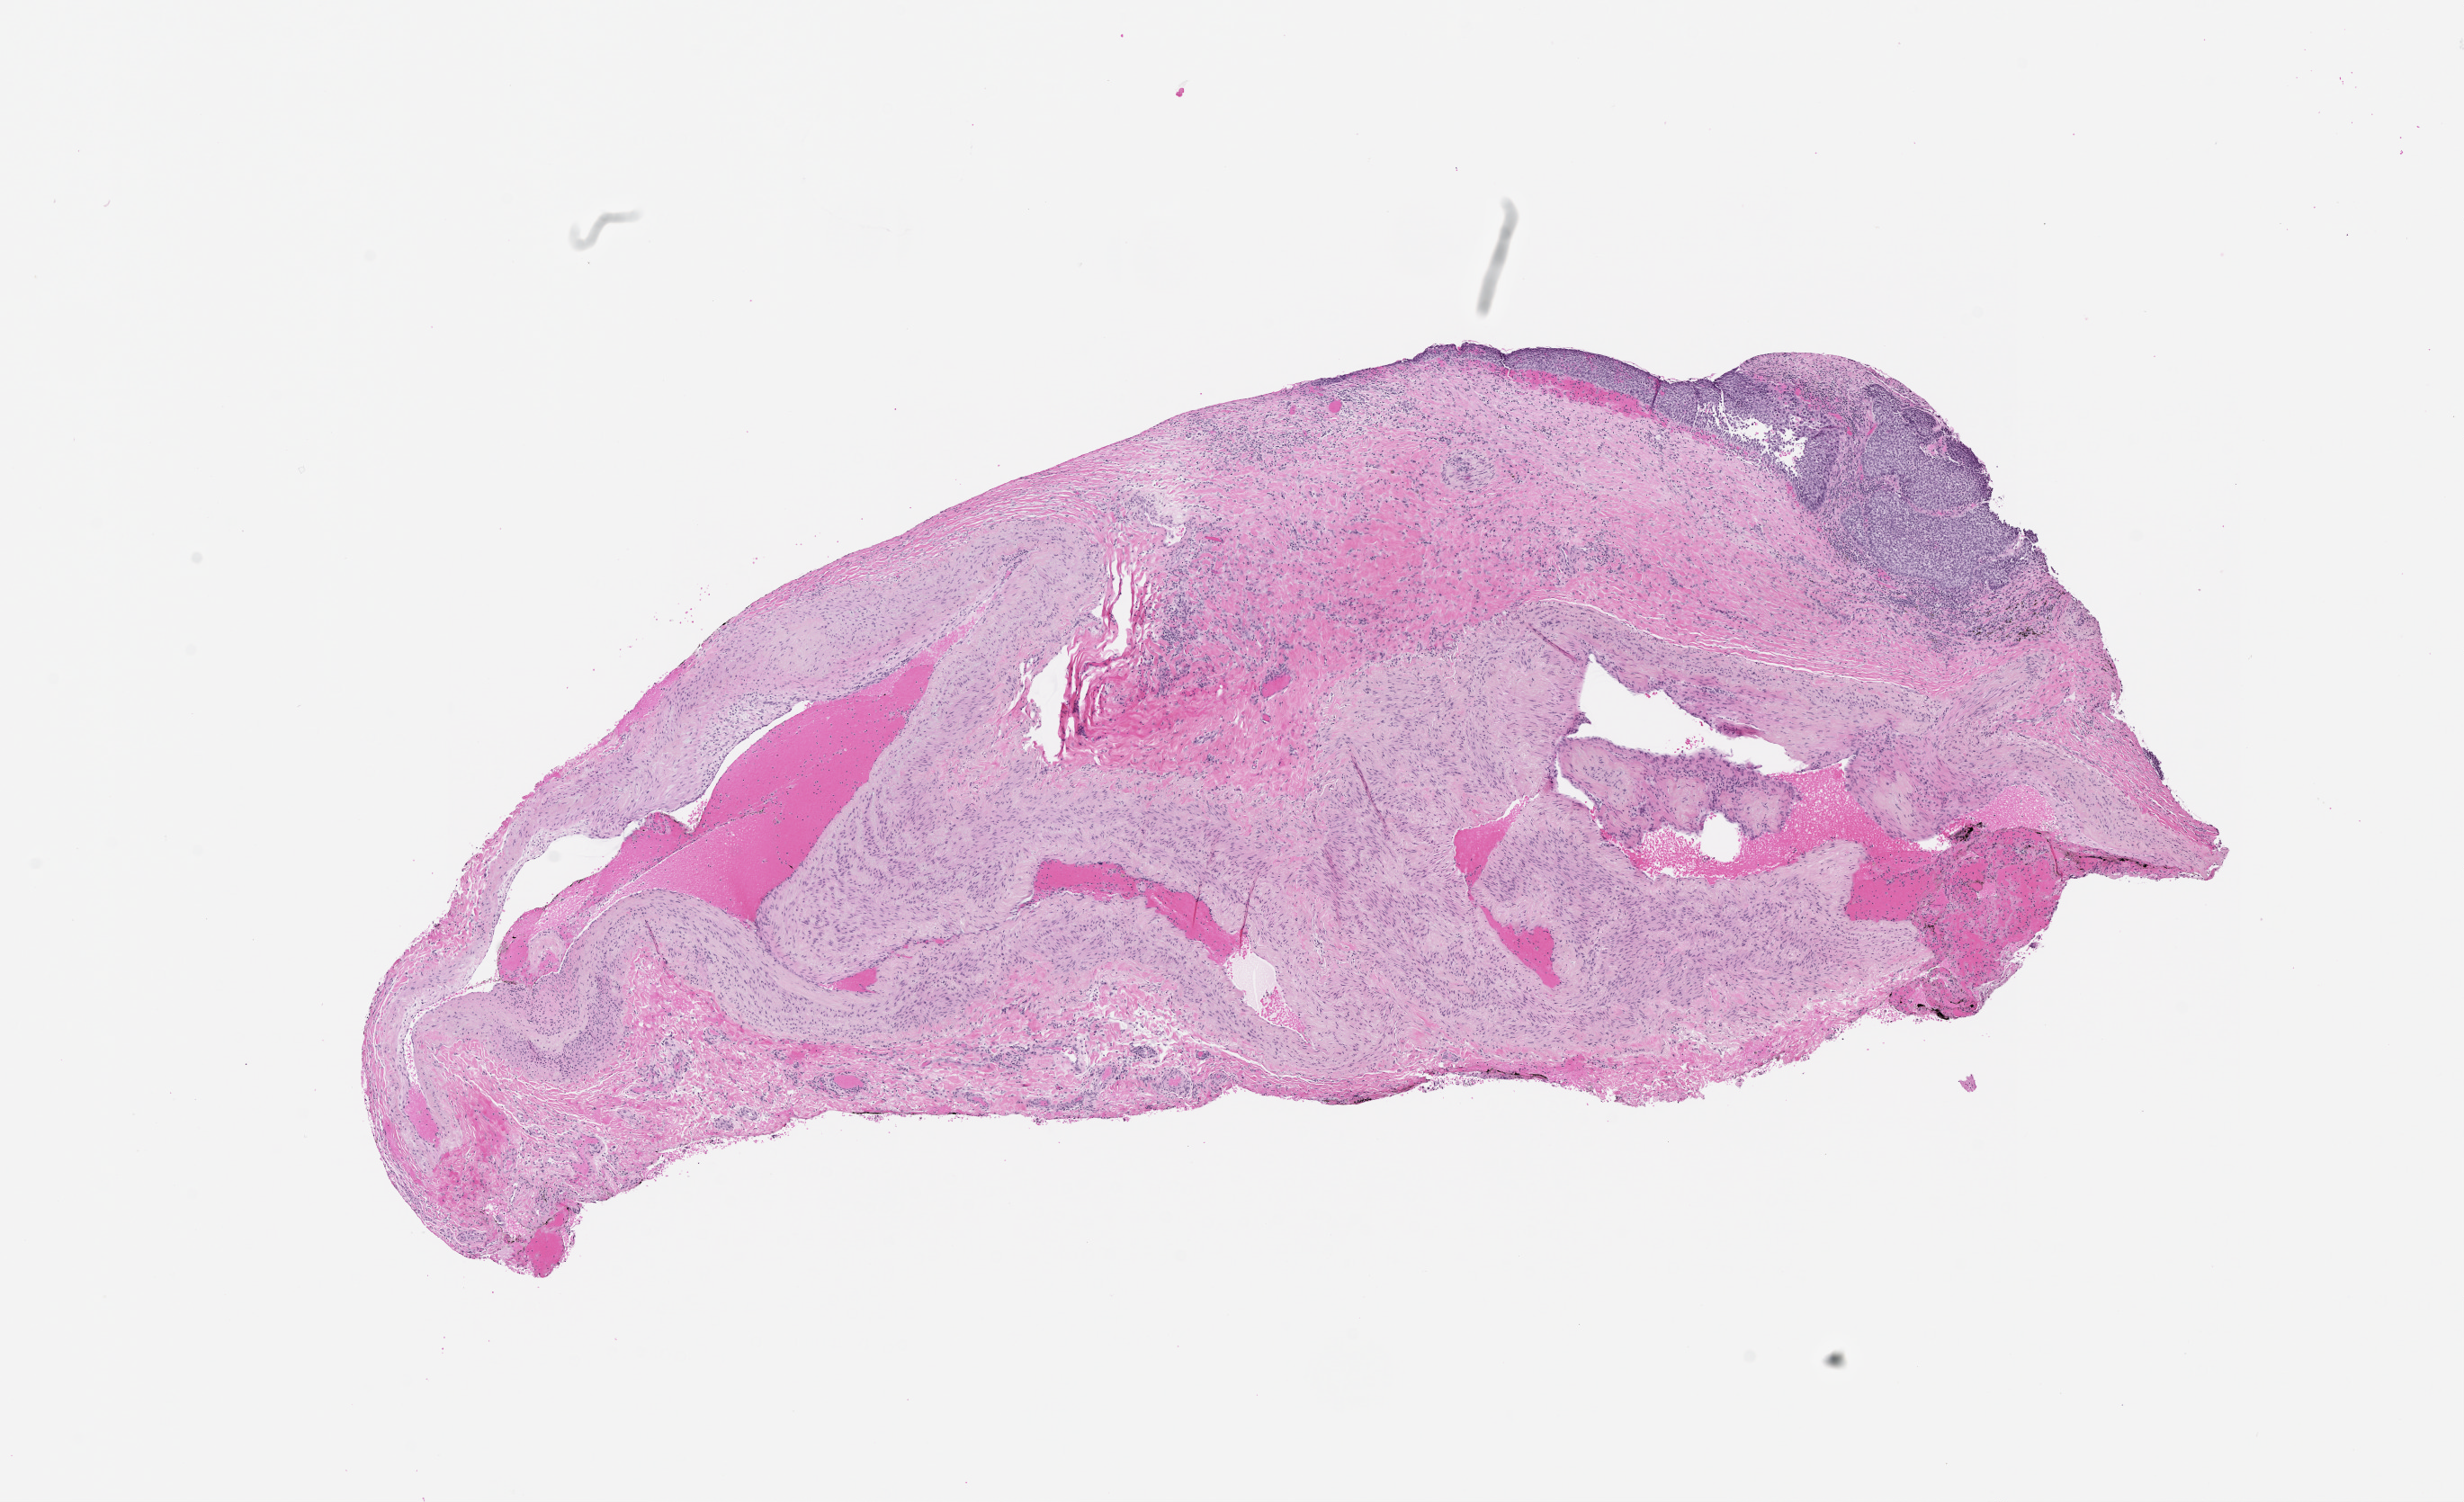
Digitized Hematoxylin and eosin (H&E) stained tissue section (whole slide), whole scanned area (about 11.0 x 6.7 mm, slide scanned at 20x) shown as a low-resolution overview, tumour tissue sample, lung. Patient: male, age 68 years.
* patient diagnosis (cohort enrolment): squamous cell carcinoma (lung)